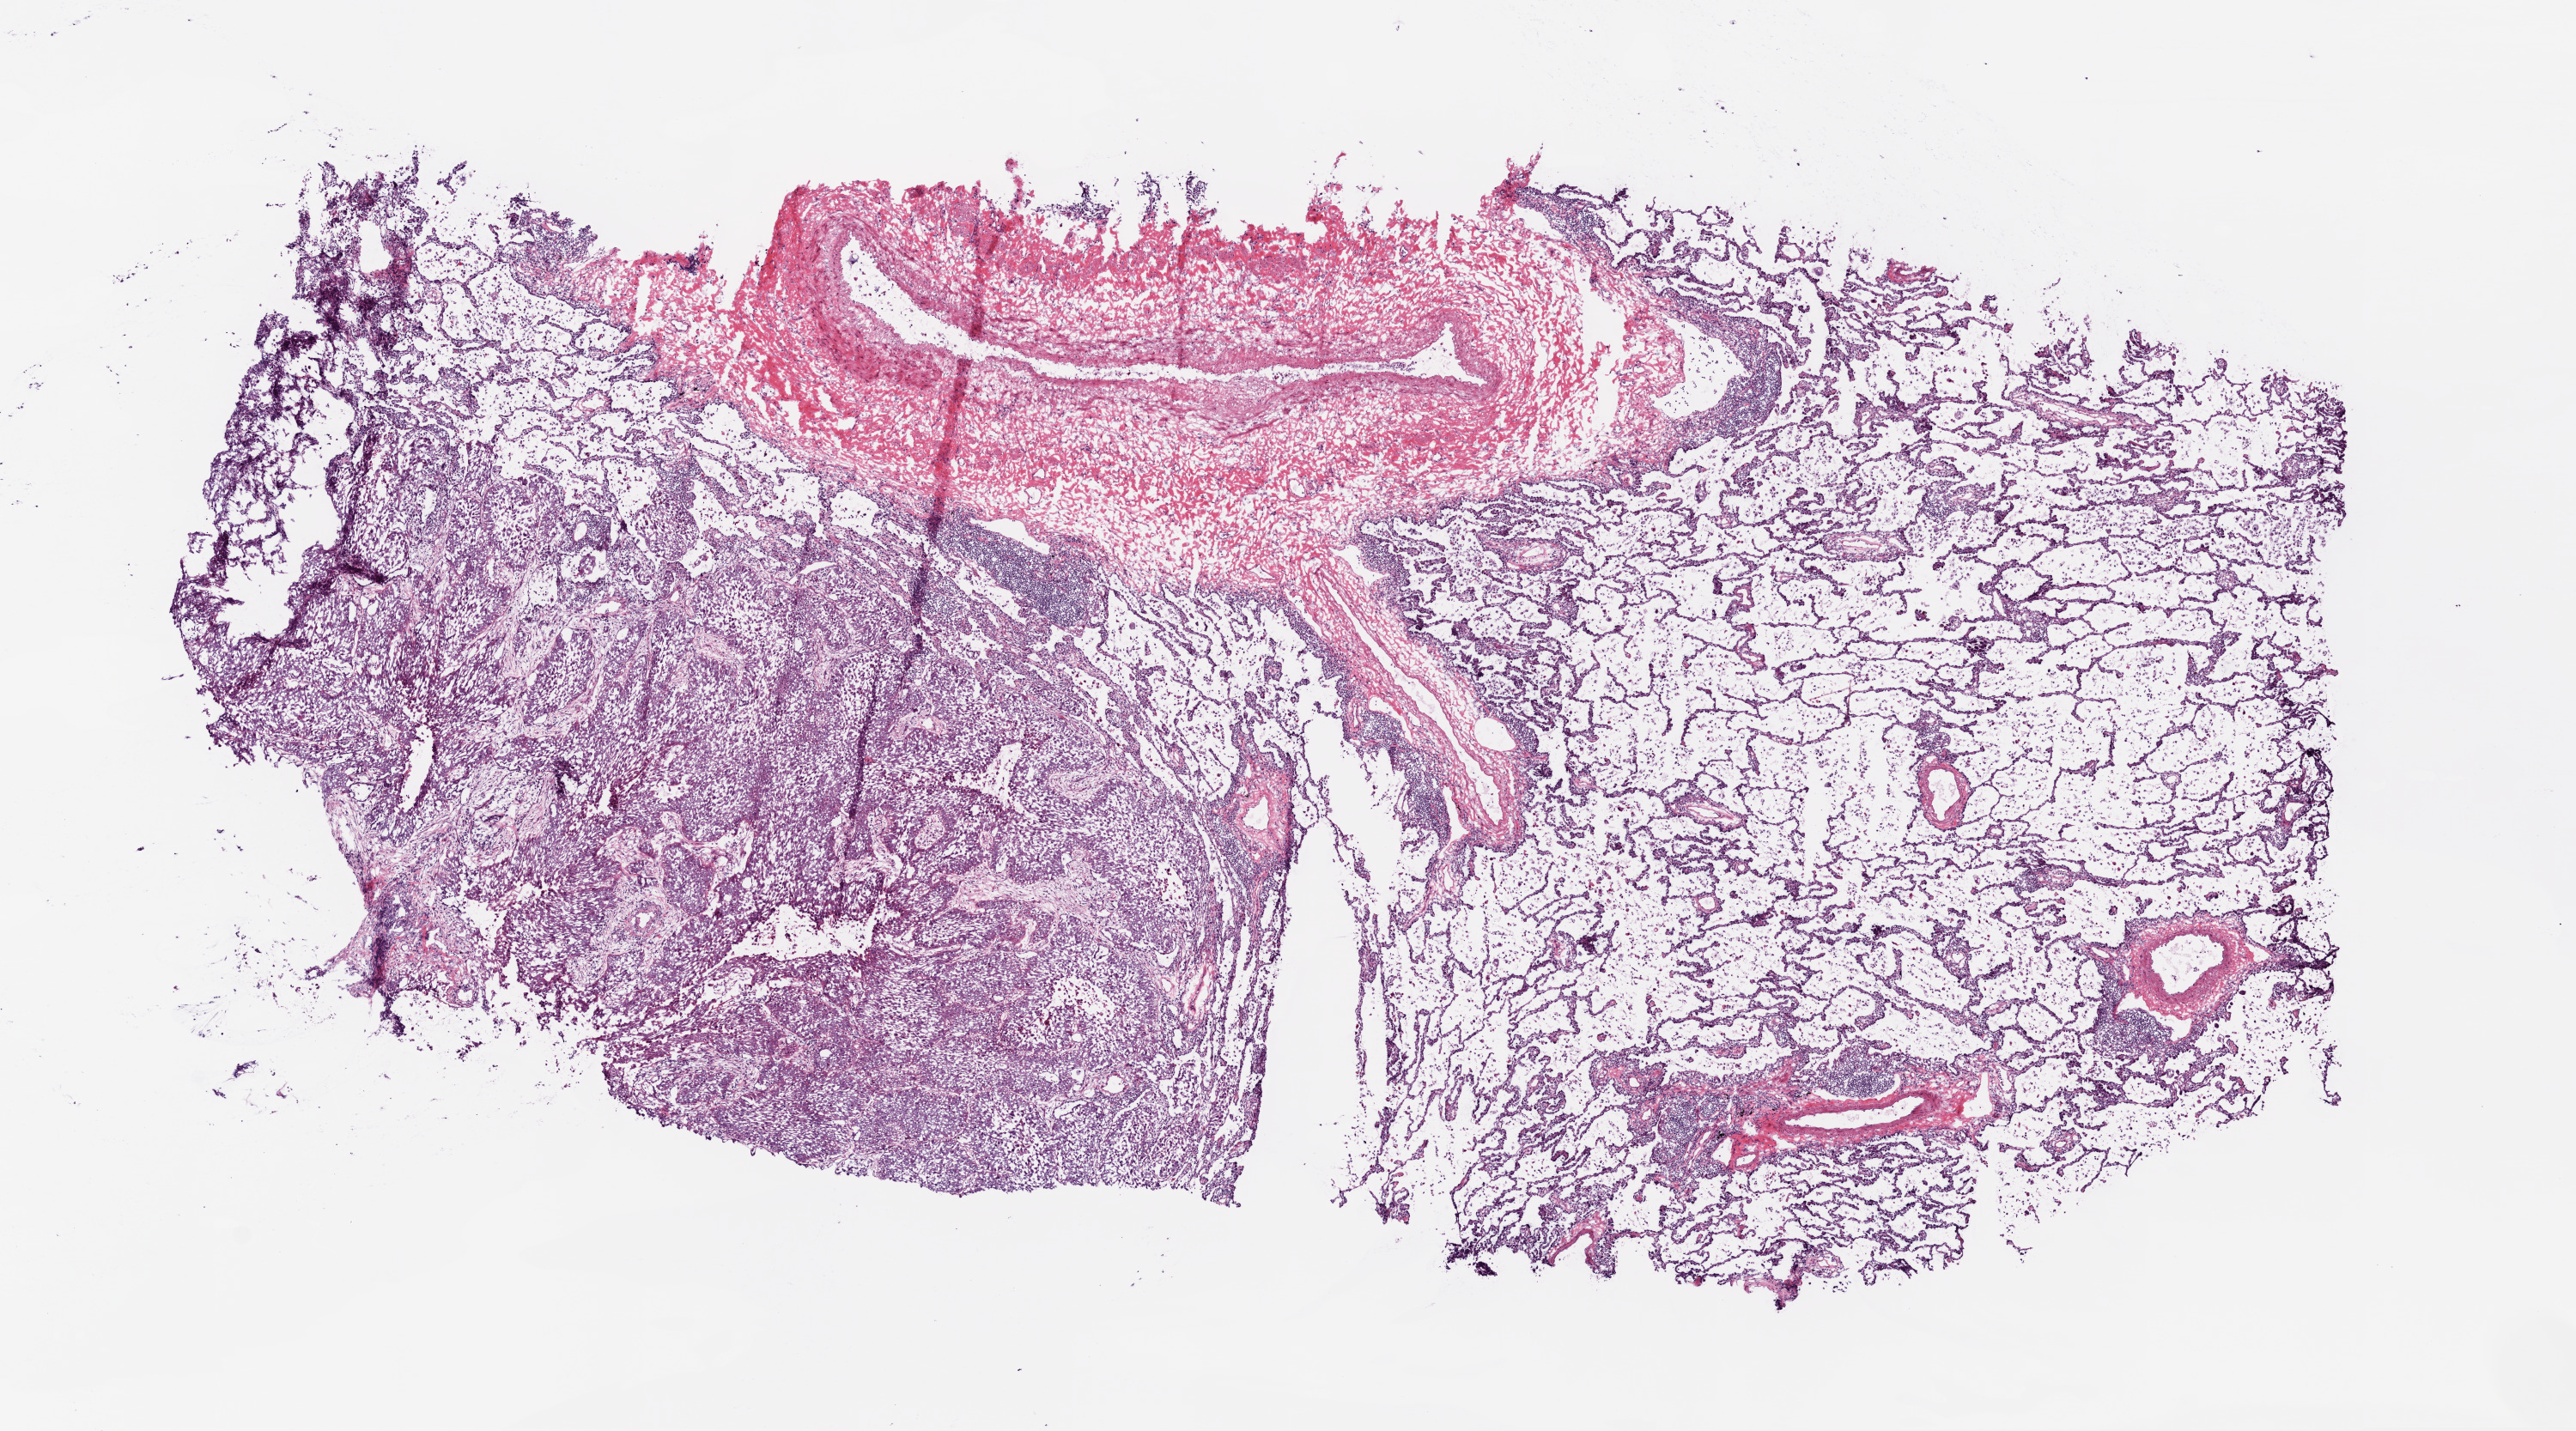
H&E whole-slide image, a low-resolution overview of the entire scanned area, about 12.0 x 6.7 mm (from a 20x scan). Frozen section from the top of the tissue portion. Sample: primary tumour, lung. Male, age 81 years at initial diagnosis. Composition of this section per pathologist review: tumour cells 70%, tumour nuclei 80%, normal cells 5%, stromal cells 5%, necrosis 20%. Inflammatory infiltration, as recorded: lymphocyte infiltration 5%, monocyte infiltration 3%.
- laterality: right
- AJCC pathologic stage: IIB
- diagnosis: Squamous cell carcinoma, NOS (lower lobe, lung)